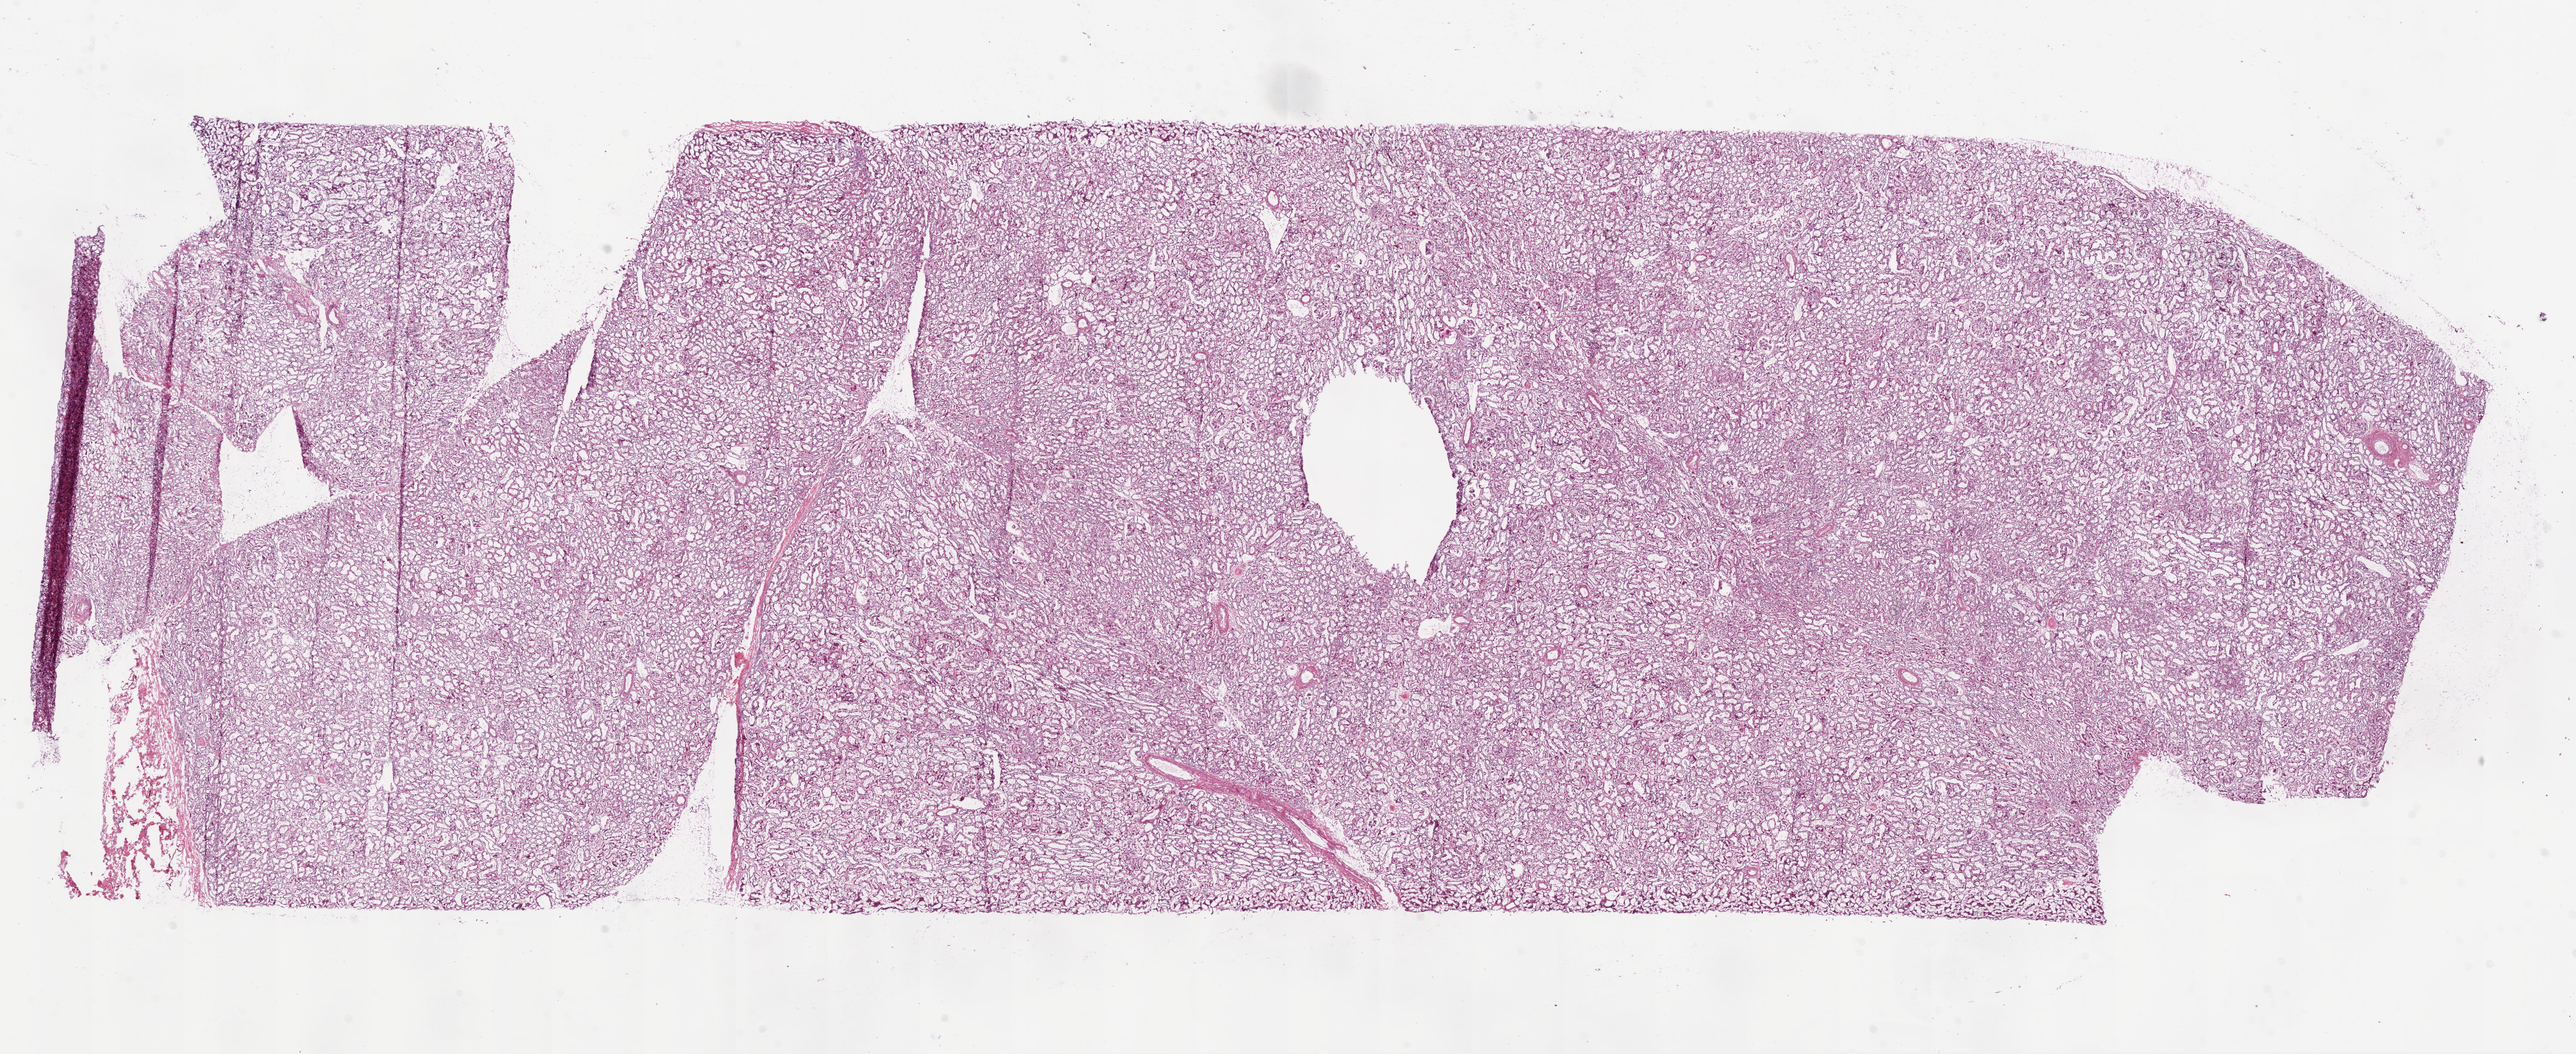
Whole-slide histology image, Hematoxylin and eosin (H&E) stained, shown as a low-resolution overview of the whole scanned area (about 28.1 x 11.5 mm); frozen section from the bottom of the tissue portion; solid tissue normal (non-tumour tissue) sample from the kidney. Female patient; age at initial diagnosis 55 years.
This section: solid tissue normal (non-tumour) sample from the same patient. Patient diagnosis: Clear cell adenocarcinoma, NOS.